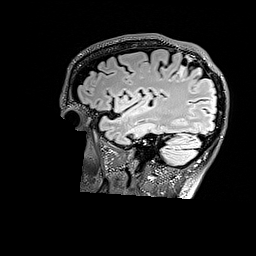
Brain MRI from a brain-tumour surgery series, one sagittal slice. T2 FLAIR. 1 mm slice thickness. 256 × 256 image matrix, field of view 256 × 256 mm. Case-level facts recorded for this patient, not image findings: histopathology: Astrocytoma; WHO grade: 3; IDH mutation: yes.
Outlined on this slice (manually delineated by an expert):
- tumour: bounding box [x1, y1, x2, y2] px = [177, 65, 187, 77]